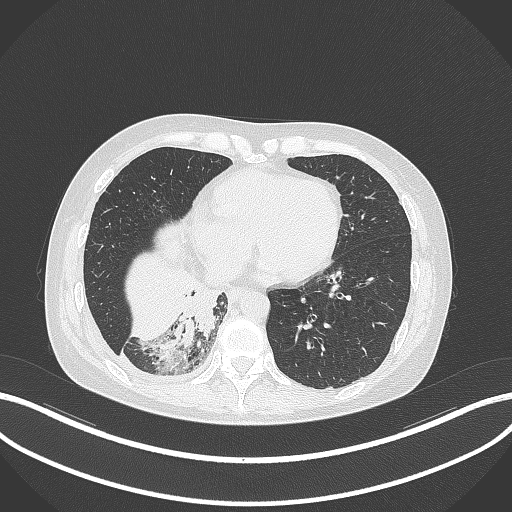
Chest CT, one axial slice. Slice 96 of 329 in the series (ordered by position). Lung window (W 1500 / L -600 HU). 1 mm slice thickness. 512 × 512 image matrix, field of view 400 × 400 mm. Female patient, age 63 years. Case-level facts recorded for this patient, not image findings: clinical TNM (as recorded): T1c N0 M0.
Structures marked on this image (bounding box drawn by a radiologist):
- lung tumour (recorded histology: adenocarcinoma): box from (x=176, y=278) to (x=219, y=350) px